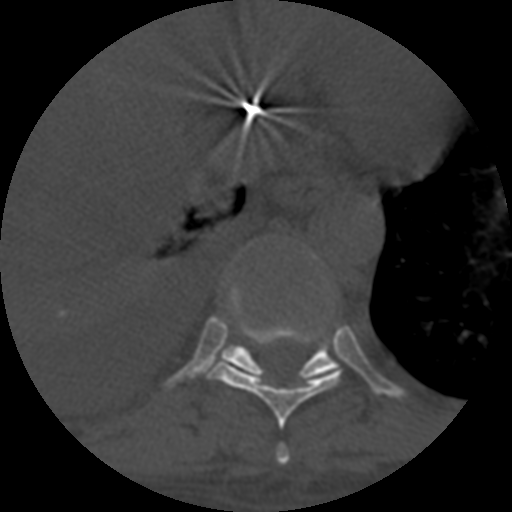
CT including the spine, one axial slice; slice 370 of 708 in the series (ordered by position); reconstruction kernel STANDARD; 120 kVp; one of 3 acquisitions stored at this slice position; bone window (W 1800 / L 400 HU); 1.25 mm slice thickness; 512 × 512 image matrix. Patient age 55 years. From the clinical record (not read from this slice): primary cancer: colon; vertebrae with lytic lesions (as recorded): T12, L1, L5.
Structures marked on this image (semi-automatic segmentation, software-assisted and operator-edited):
- T10 vertebra: box from (x=221, y=255) to (x=340, y=381) px
- T8 vertebra: (x=275, y=445)–(x=290, y=465)
- T9 vertebra: (x=207, y=289)–(x=343, y=428)